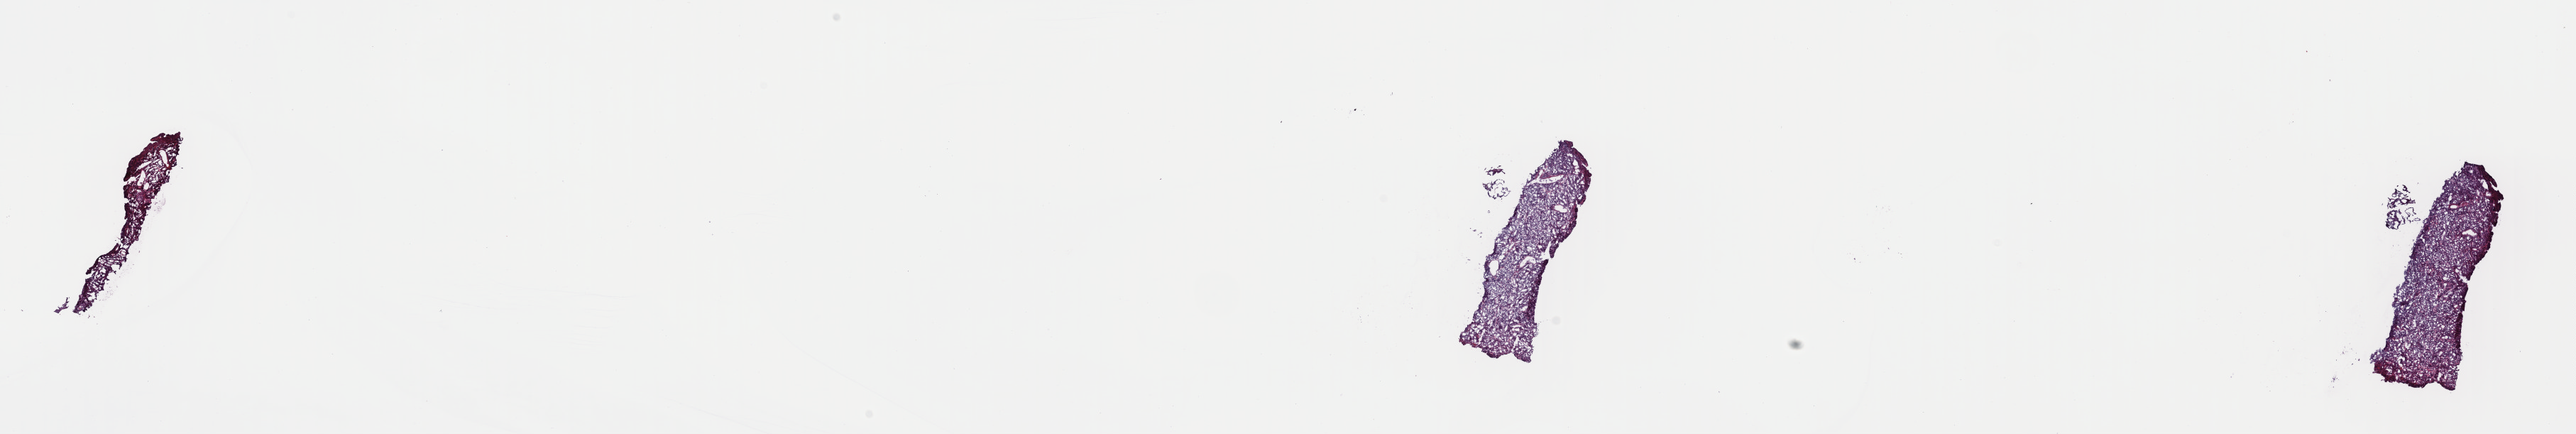
Hematoxylin and eosin (H&E) stained whole-slide image — low-resolution overview of the scanned area, about 28.6 x 4.8 mm. Frozen section. Primary tumour sample from the cervix. Patient: female, age at initial diagnosis 35 years.
Pathologic diagnosis: Squamous cell carcinoma, NOS (cervix uteri).